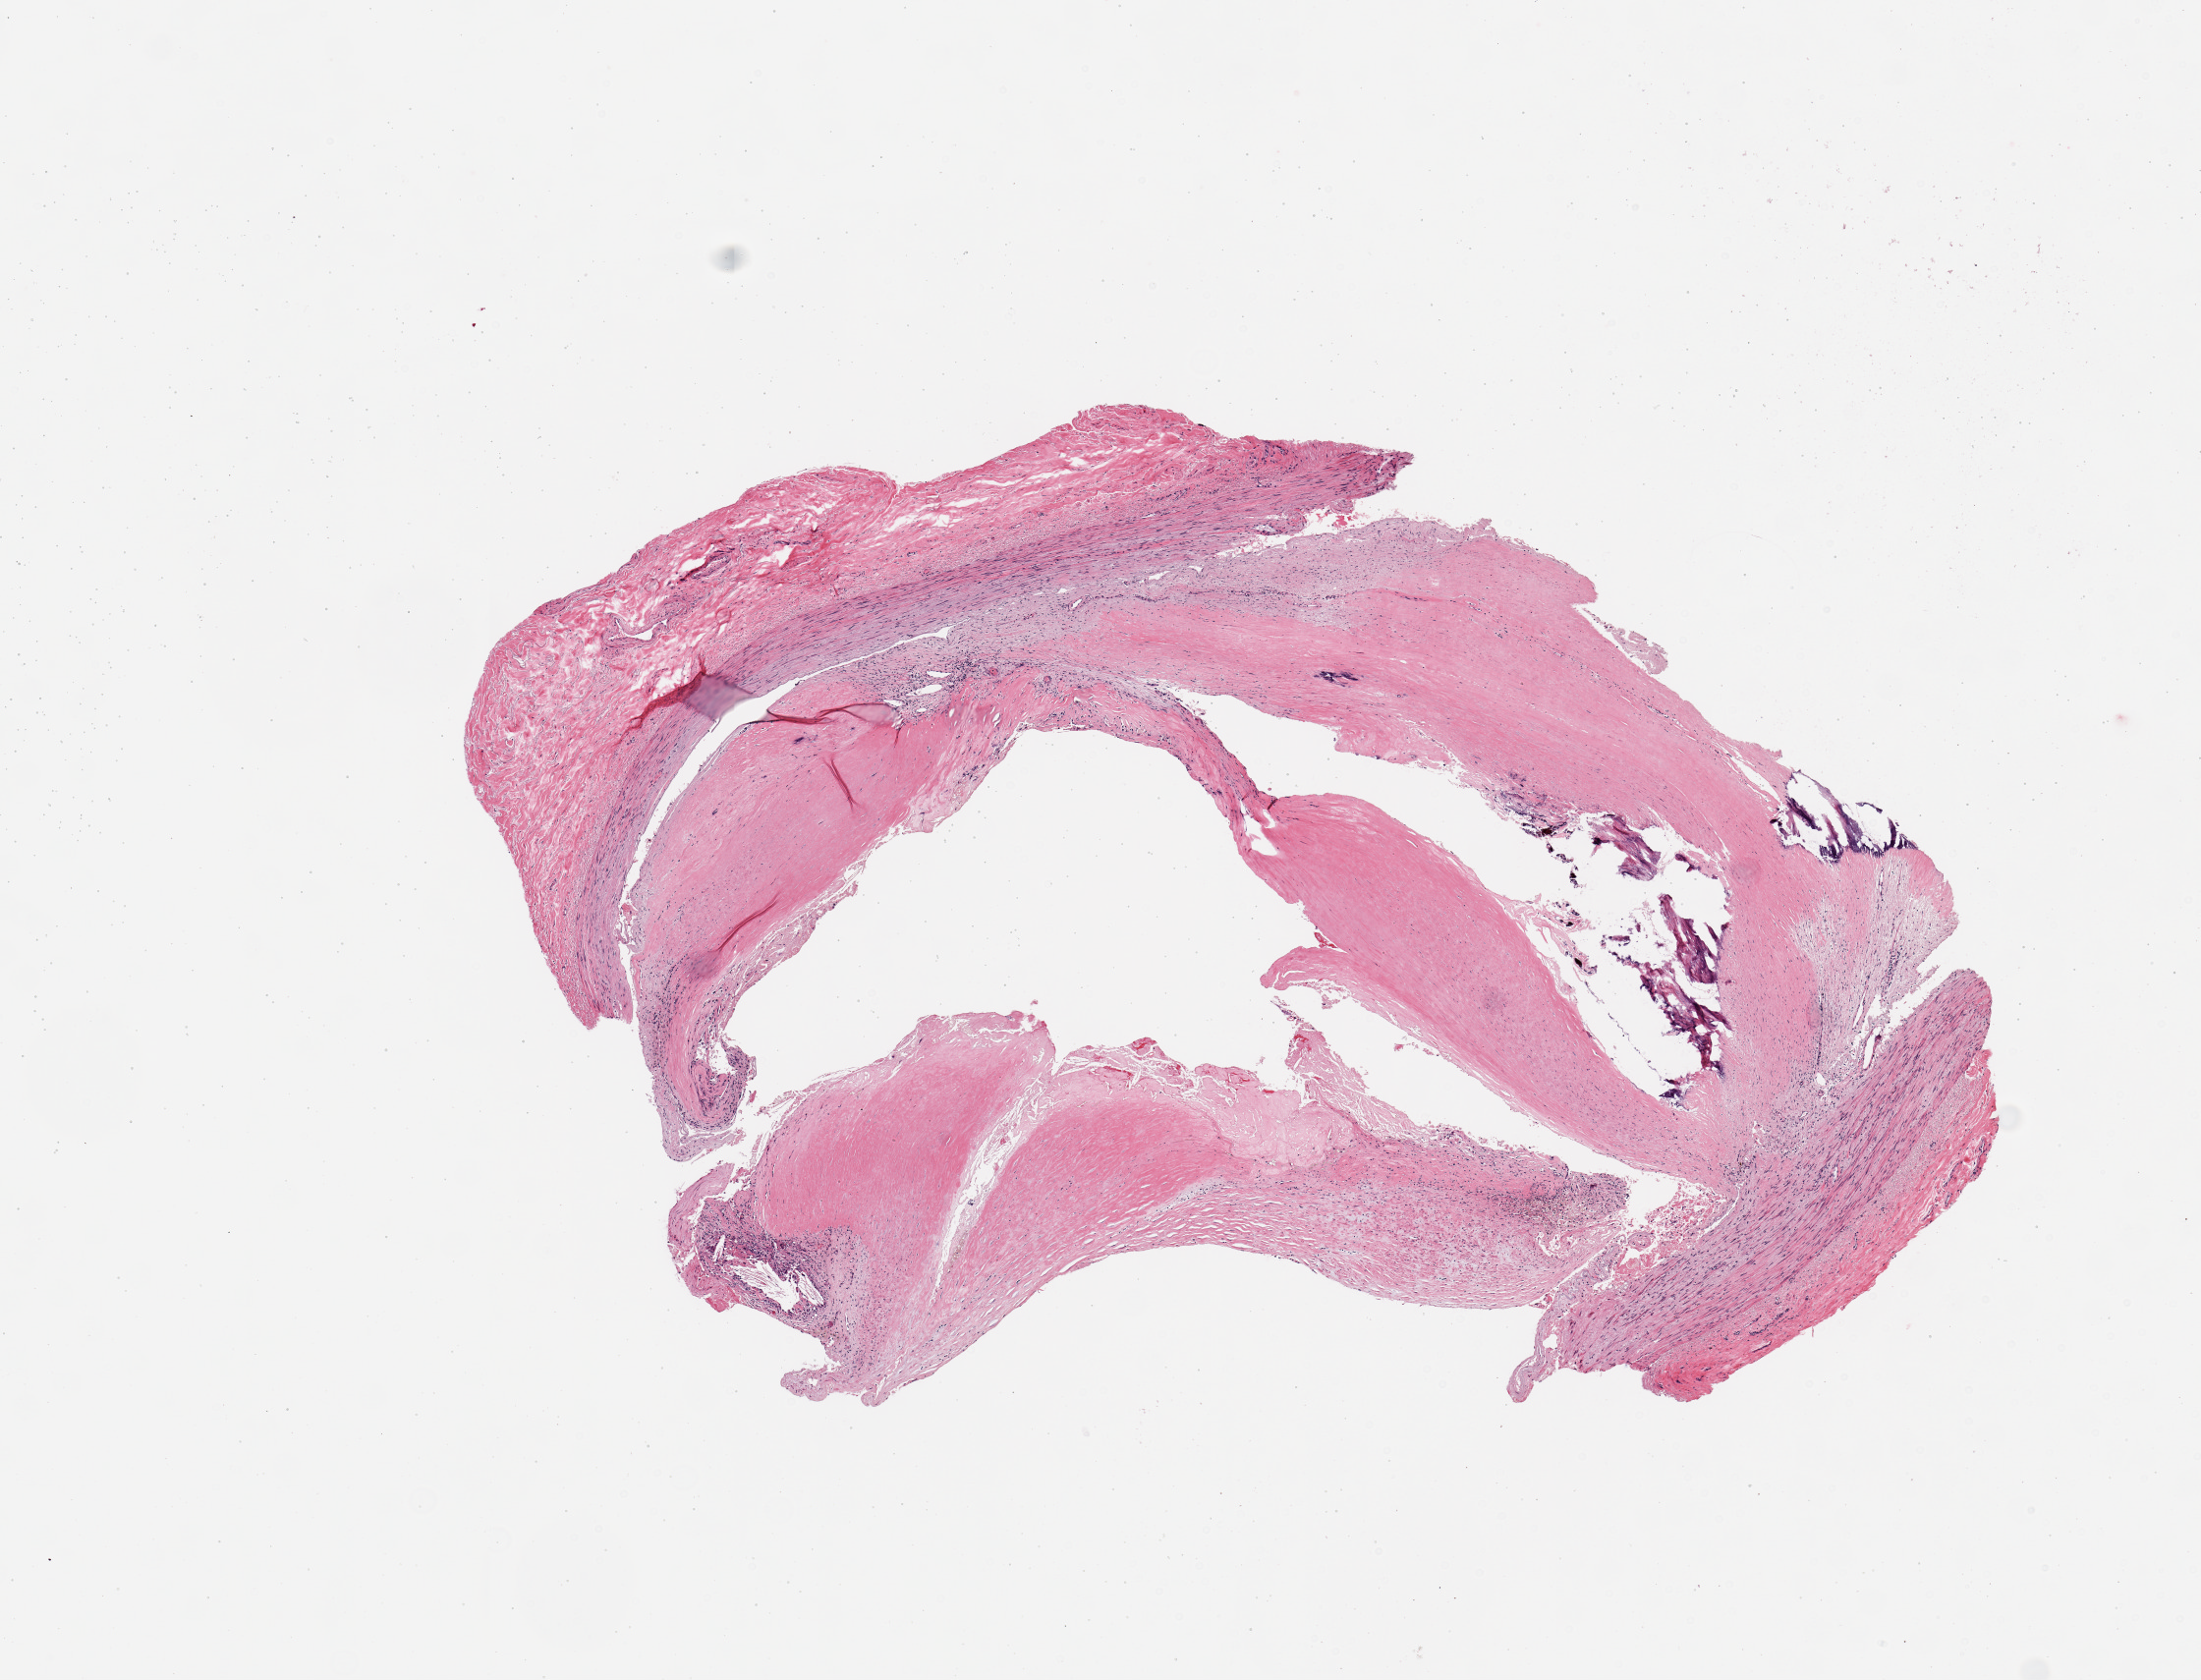
H&E whole-slide image, brightfield, low-resolution overview of the scanned area, about 8.9 x 6.8 mm, PAXgene-fixed paraffin-embedded (PFPE) section, target tissue: tibial artery, tissue donor sample. Donor sex: male.
* review note (as recorded): 1 piece, lumen subtotally occluded with focally calcified atheromatous deposits